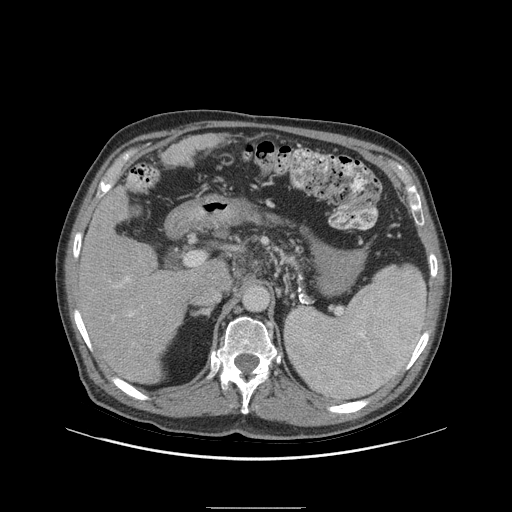
Contrast-enhanced abdominal CT (liver protocol), one axial slice; 140 kVp; soft-tissue window (W 400 / L 40 HU); 512 × 512 image matrix, field of view 440 × 440 mm. Case-level facts recorded for this patient, not image findings: diagnosis: hepatocellular carcinoma (patient treated with transarterial chemoembolisation; whether this scan precedes or follows treatment is not stated here); TNM stage (as recorded): Stage-I; Child-Pugh class: A; tumour nodularity: uninodular.
Annotated regions visible in this slice (semi-automatically segmented with operator editing):
- liver parenchyma outside the tumour (the mass and vessels are separate outlines, so this box may not span the whole liver): bounding box (x1, y1, x2, y2) in pixels: (74, 186, 200, 384)
- liver vessels: (117, 277, 133, 317)